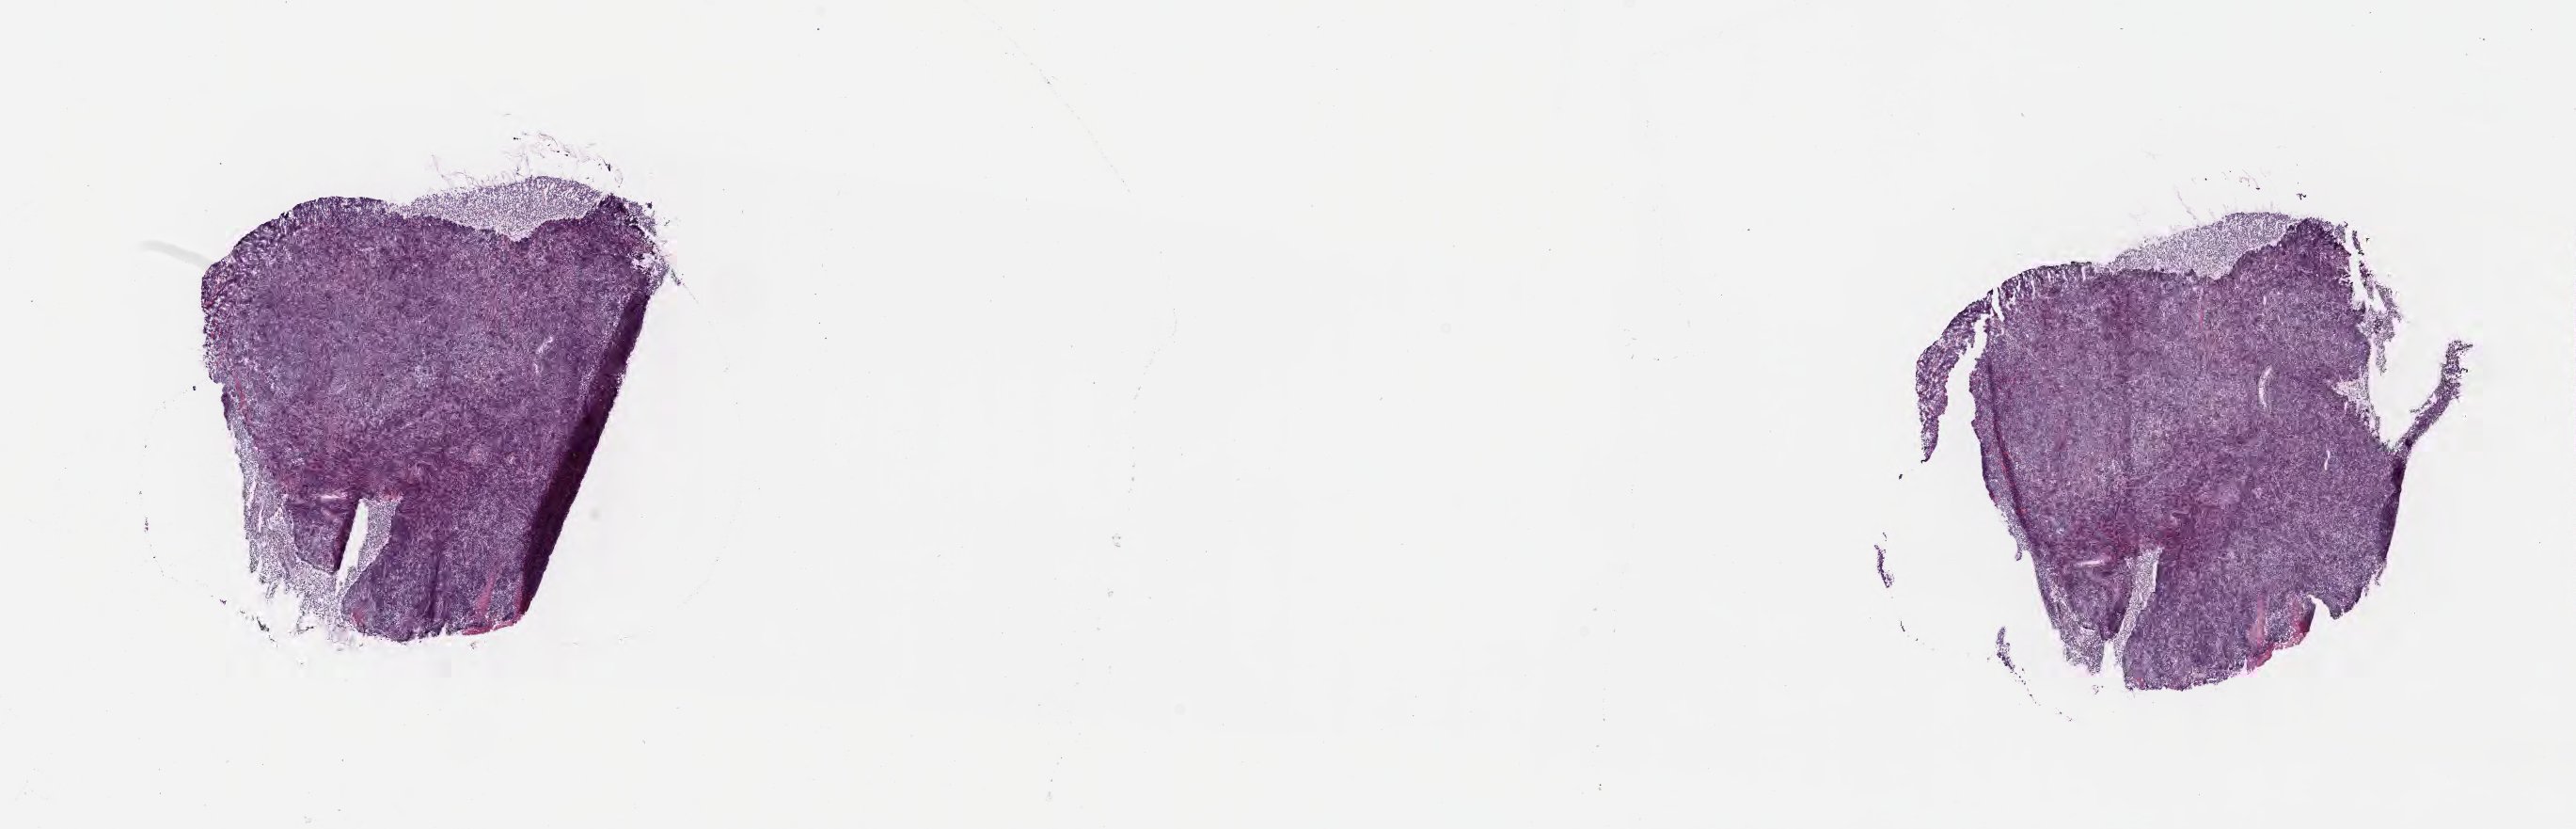
Digitized haematoxylin and eosin-stained section — shown as a low-resolution overview of the whole scanned area (about 22.1 x 7.1 mm), cryosection, primary tumor, anatomic site: cranium. Male, age 8 years at initial diagnosis. Pathologist review of this section (percent, as recorded): tumor cells 90%, tumor nuclei 90%, stromal cells 5%, necrosis 5%, normal cells 0%. Infiltration values recorded for this section: lymphocyte infiltration 50%, monocyte infiltration 30%, neutrophil infiltration 5%.
Section: top of the tissue portion. Diagnosis: Diffuse large B-cell lymphoma, NOS. Ann Arbor stage (patient): Stage I.